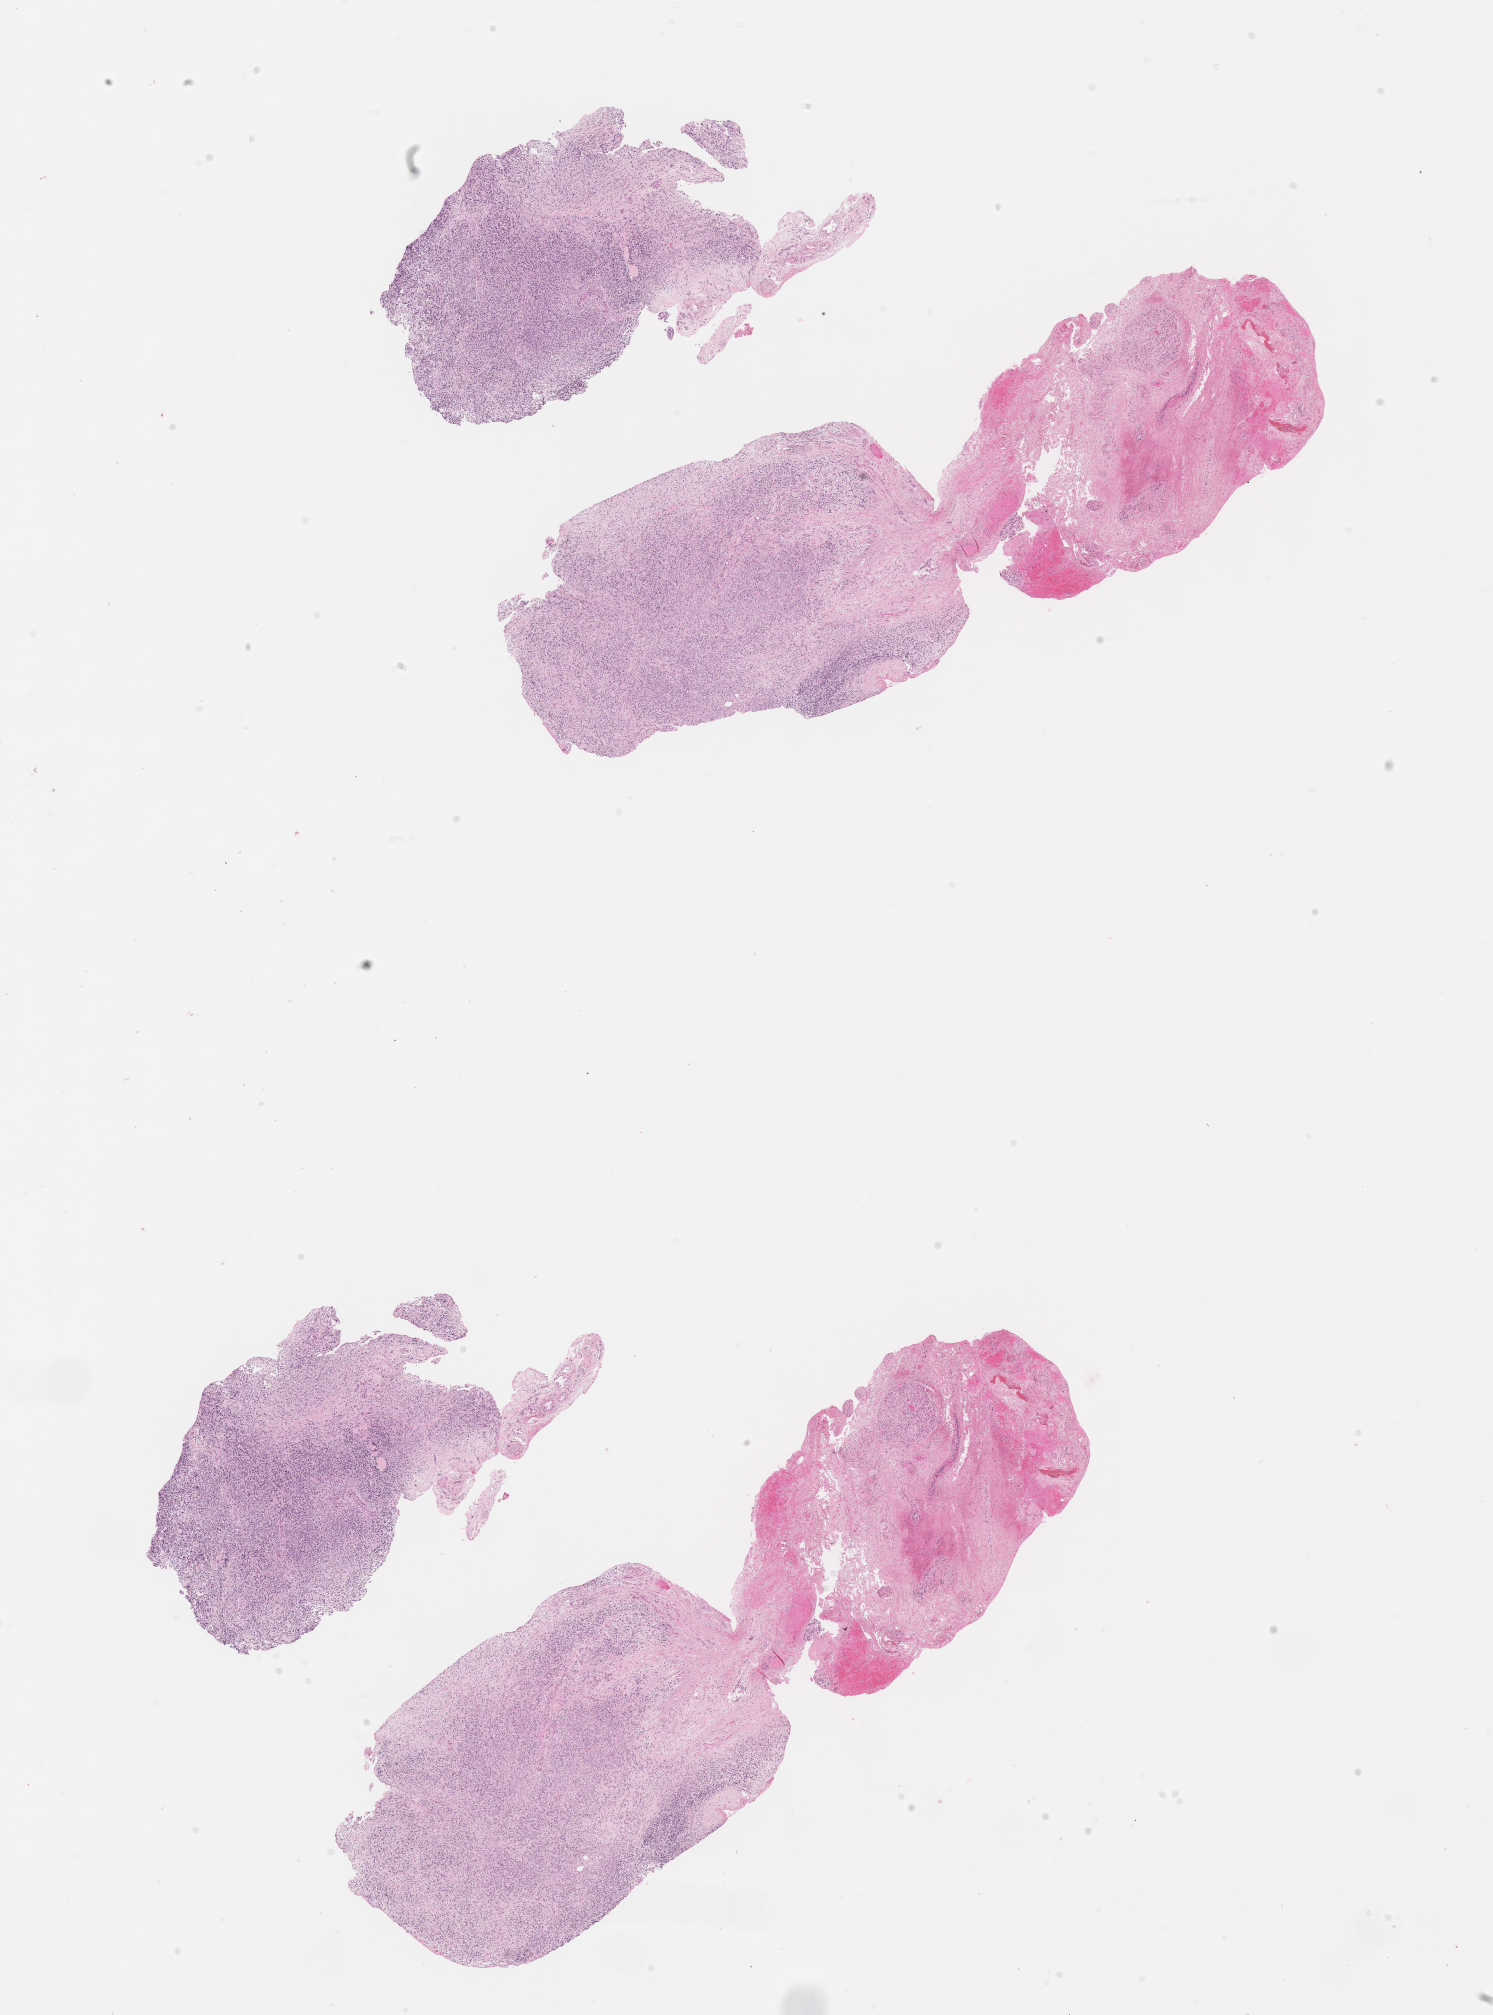
Whole-slide image, haematoxylin and eosin stain of tumor tissue — whole scanned area (about 12.1 x 16.3 mm) shown as a low-resolution overview. Formalin-fixed, paraffin-embedded (FFPE) tissue. Sample anatomic site: pelvis. Male patient, age at diagnosis 0.3 years.
Metastatic status at presentation (as recorded): non-metastatic. Stage (as recorded): 3. Diagnosis: rhabdomyosarcoma; histological classification: embryonal rhabdomyosarcoma.